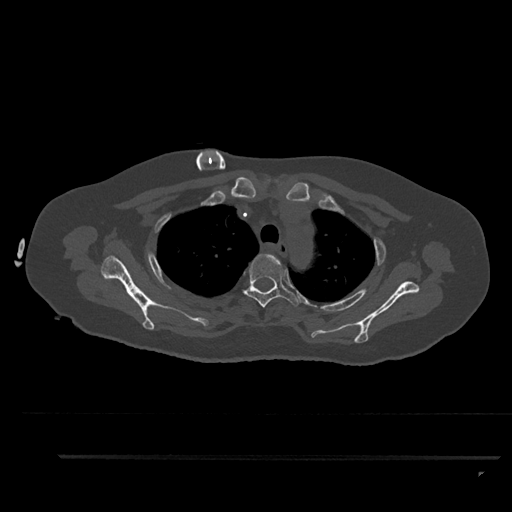
CT including the spine, one axial slice. Position 687 of 797 along the scan axis. Reconstruction kernel Br40s/3. 120 kVp. Bone window (W 1800 / L 400 HU). 0.5 mm slice thickness. 512 × 512 image matrix, field of view 408 × 408 mm. Patient: female, 44 years. From the clinical record (not read from this slice): primary cancer: renal; vertebrae with lytic lesions (as recorded): L1.
Outlined on this slice (semi-automatic segmentation, software-assisted and operator-edited):
- T3 vertebra: bounding box <242,254,300,308> (left, top, right, bottom; pixels)